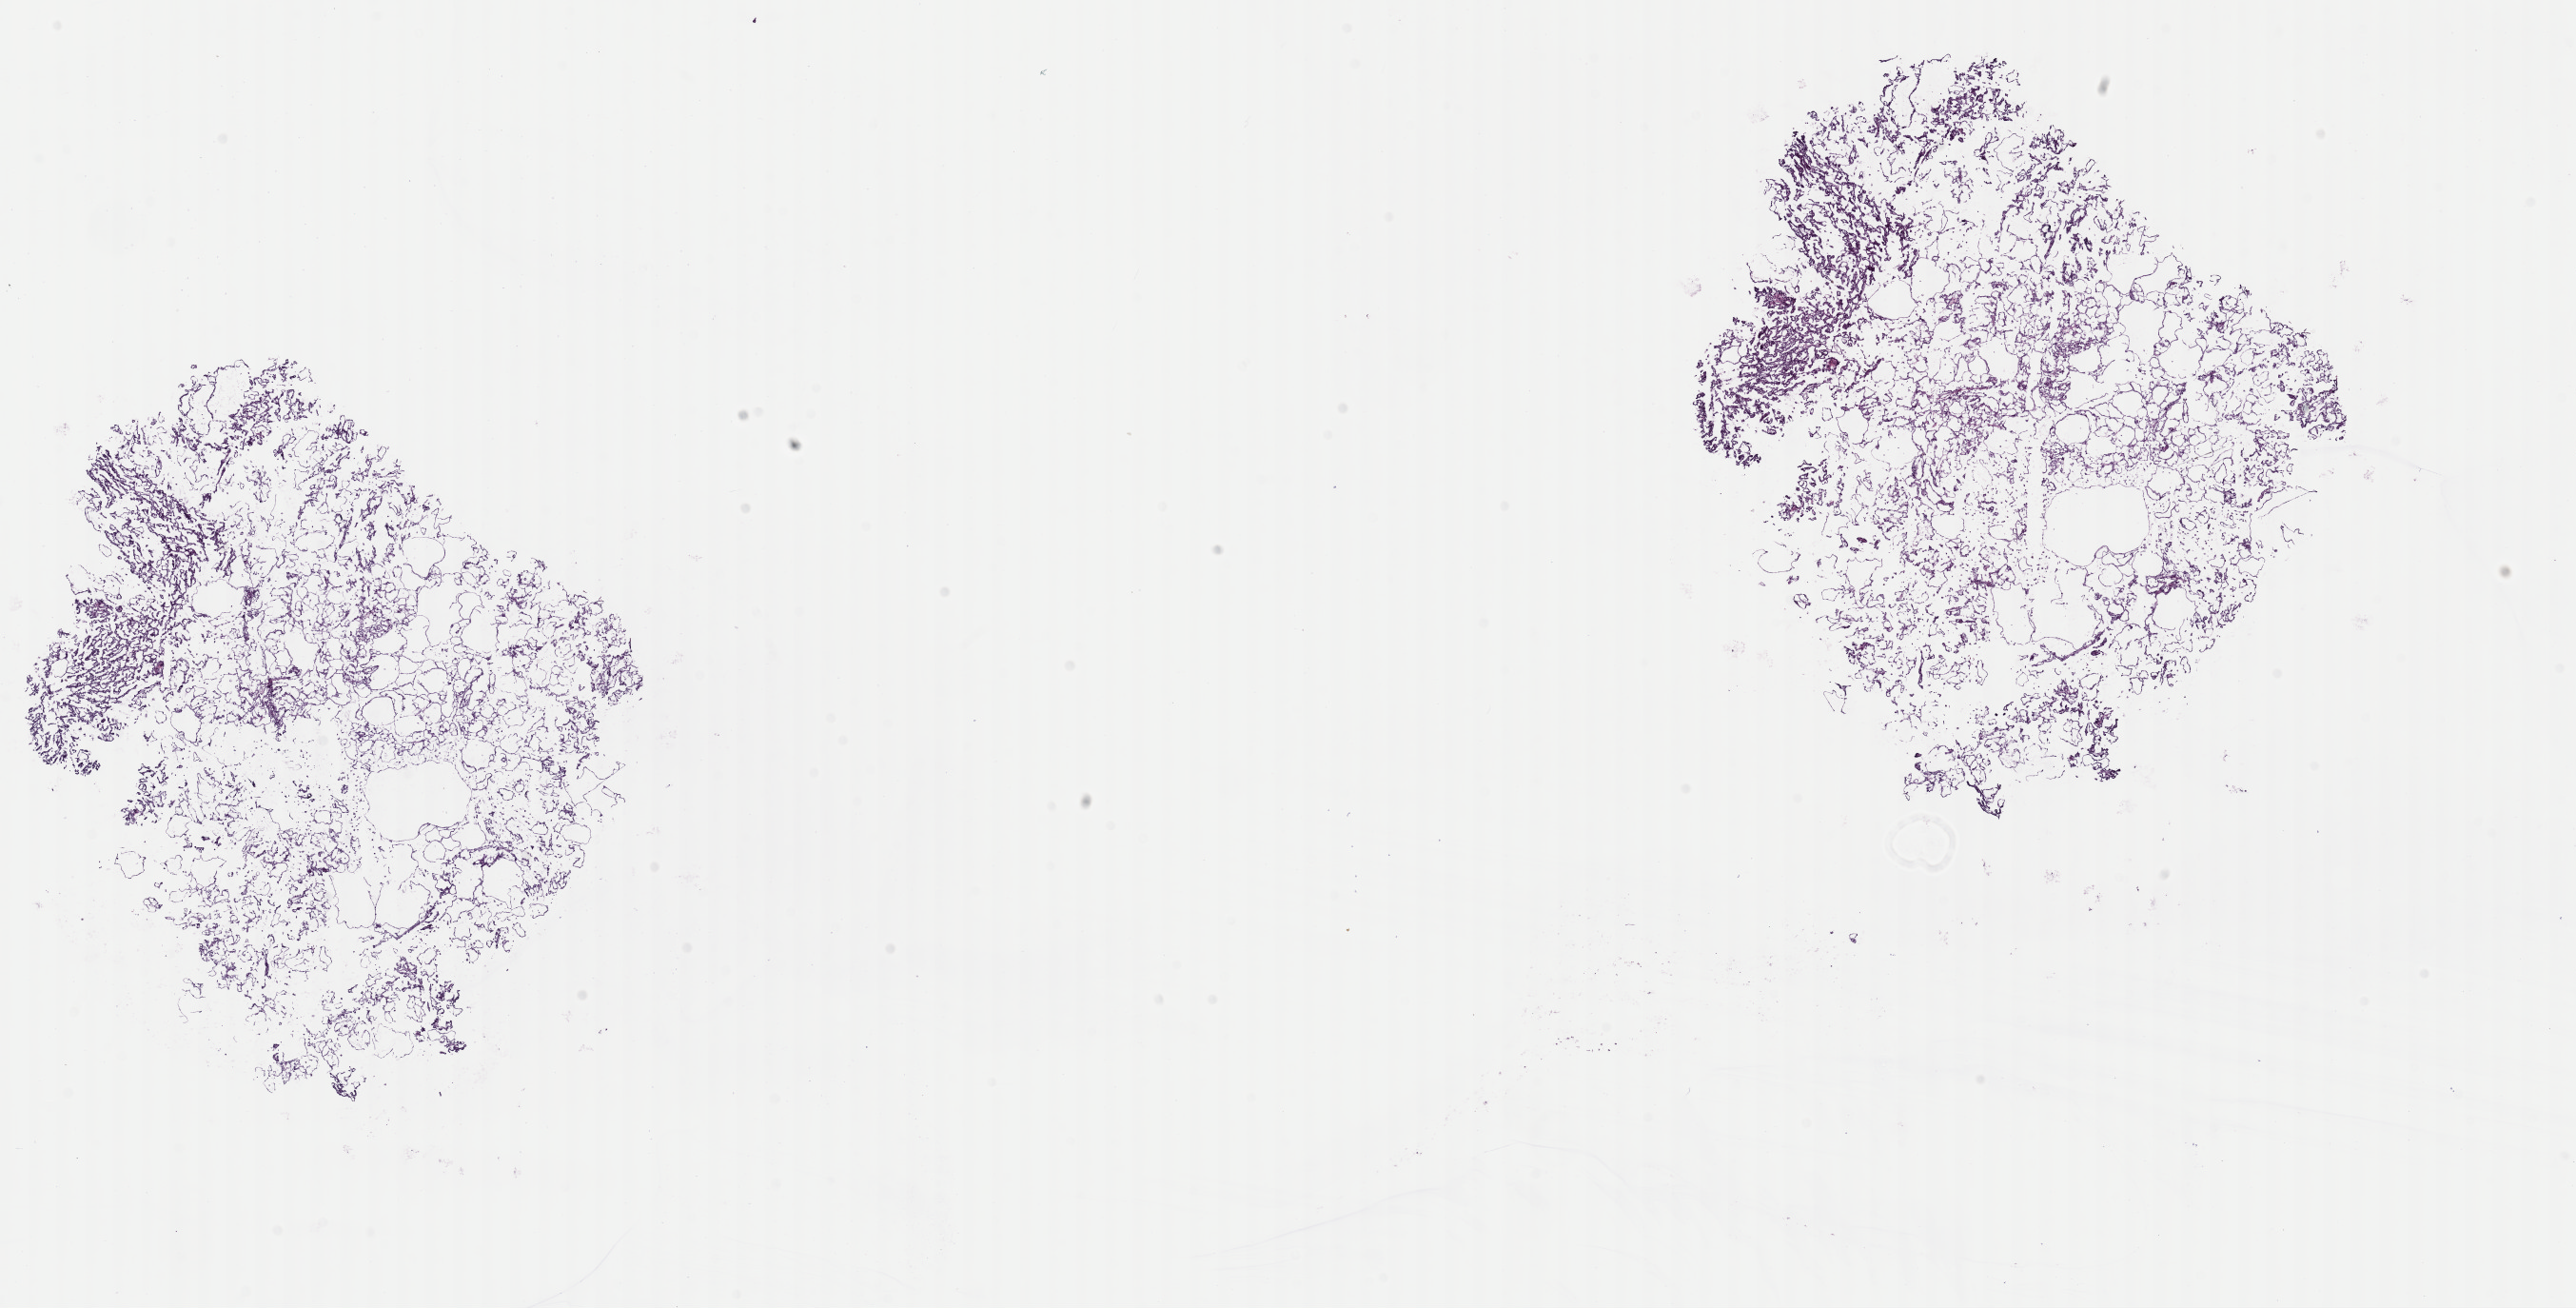
Whole-slide histology image, H&E-stained, a low-resolution overview of the entire scanned area, about 21.4 x 10.9 mm, frozen section from the top of the tissue portion, primary tumour sample from the kidney. Male patient; age at initial diagnosis 79 years. Pathologist review of this section (percent, as recorded): tumour cells 90%, tumour nuclei 90%, normal cells 0%, stromal cells 10%, necrosis 0%. Infiltration values recorded for this section: lymphocyte infiltration 0%, monocyte infiltration 0%, neutrophil infiltration 0%.
TNM: T3c N0 MX. AJCC pathologic stage: III. Pathologic diagnosis: Papillary adenocarcinoma, NOS.